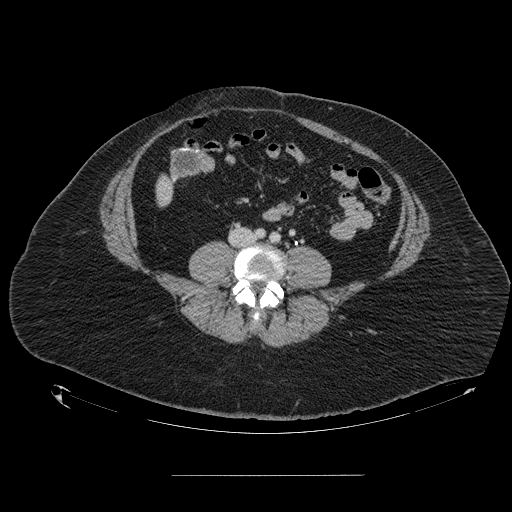
Contrast-enhanced abdominal CT, one axial slice; position 9 of 164 along the scan axis; 120 kVp; intravenous contrast given; soft-tissue window (W 400 / L 40 HU); 2.5 mm slice thickness; 512 × 512 image matrix, field of view 495 × 495 mm. Female patient, age 52 years. From the clinical record (not read from this slice): diagnosis: colorectal cancer liver metastases, imaged before liver resection; multiple liver metastases: yes; largest metastasis: 3.5 cm; disease in both lobes: no.
Structures marked on this image (expert manual segmentation):
- liver: box from (x=157, y=177) to (x=174, y=204) px